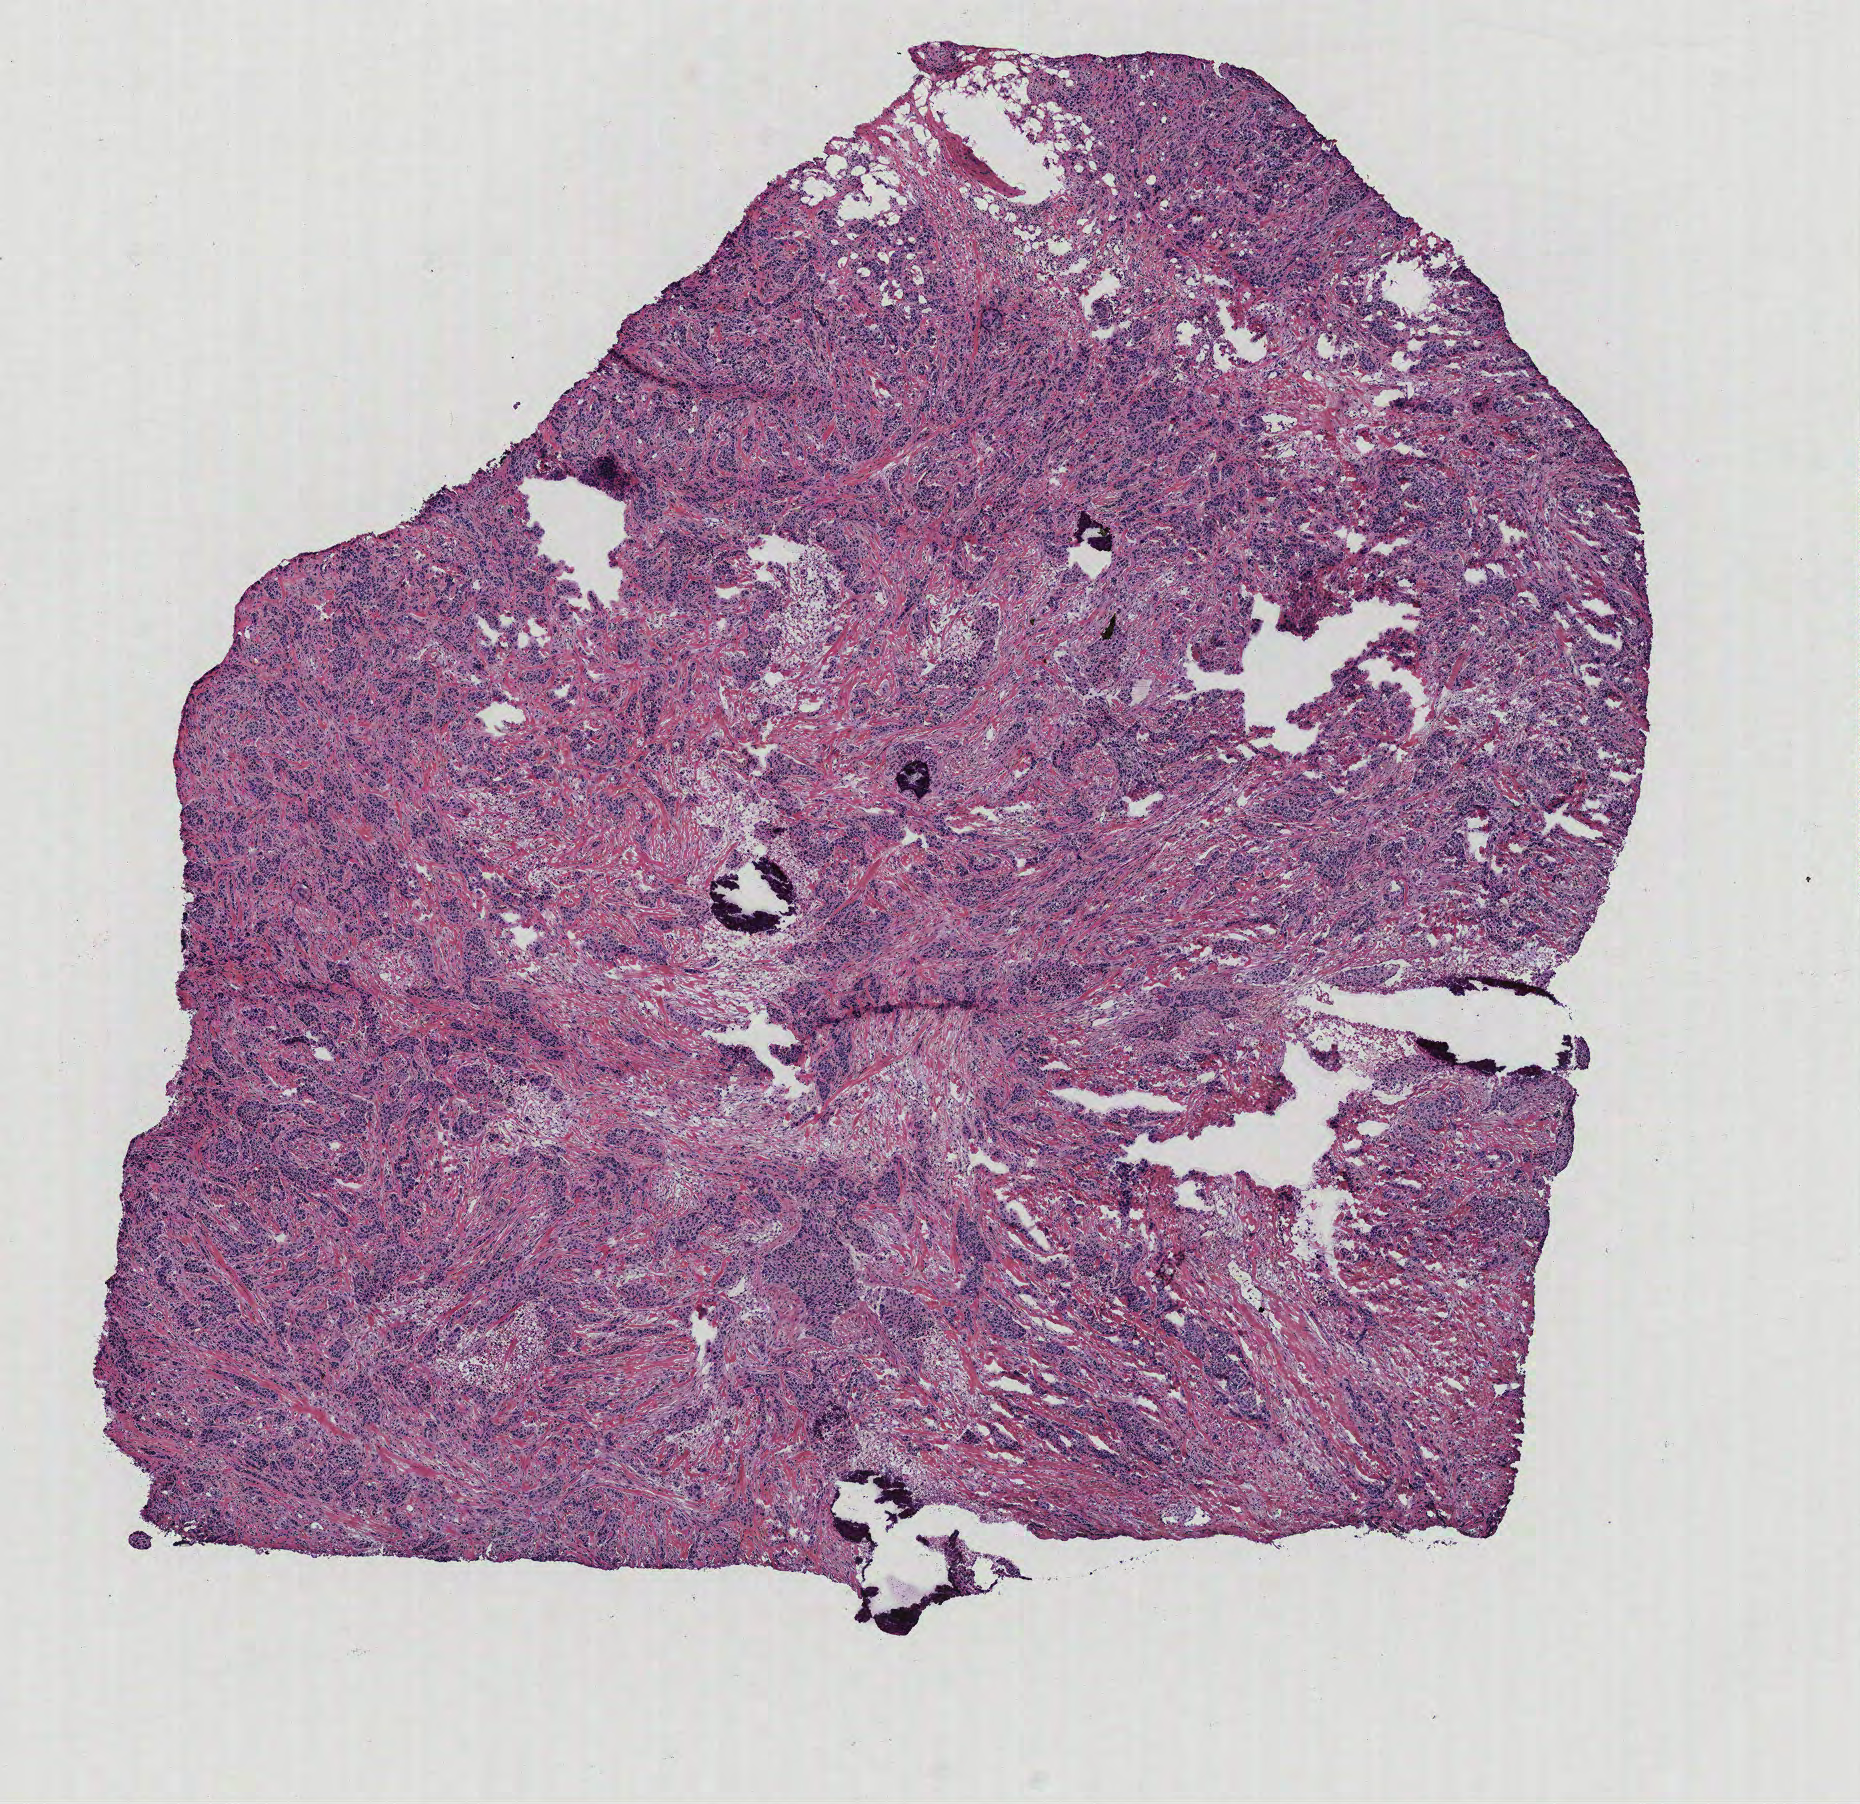
Hematoxylin and eosin (H&E) stained whole-slide image — whole scanned area (about 7.4 x 7.2 mm, slide scanned at 40x) shown as a low-resolution overview; breast, tissue type not recorded. 47-year-old female patient.
Patient diagnosis: Infiltrating duct carcinoma, NOS.